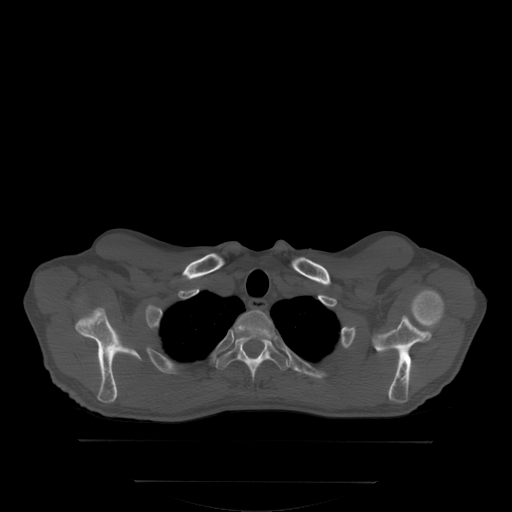
CT including the spine, one axial slice. Slice 281 of 350 in the series (ordered by position). Bone window (W 1800 / L 400 HU). 2.5 mm slice thickness. 512 × 512 image matrix, field of view 500 × 500 mm. Male patient, age 58 years. Case-level facts recorded for this patient, not image findings: primary cancer: prostate.
Outlined on this slice (semi-automatic segmentation, software-assisted and operator-edited):
- T1 vertebra: bounding box [x1, y1, x2, y2] px = [234, 309, 276, 351]
- T2 vertebra: [214, 334, 290, 377]
- T3 vertebra: [214, 354, 289, 362]